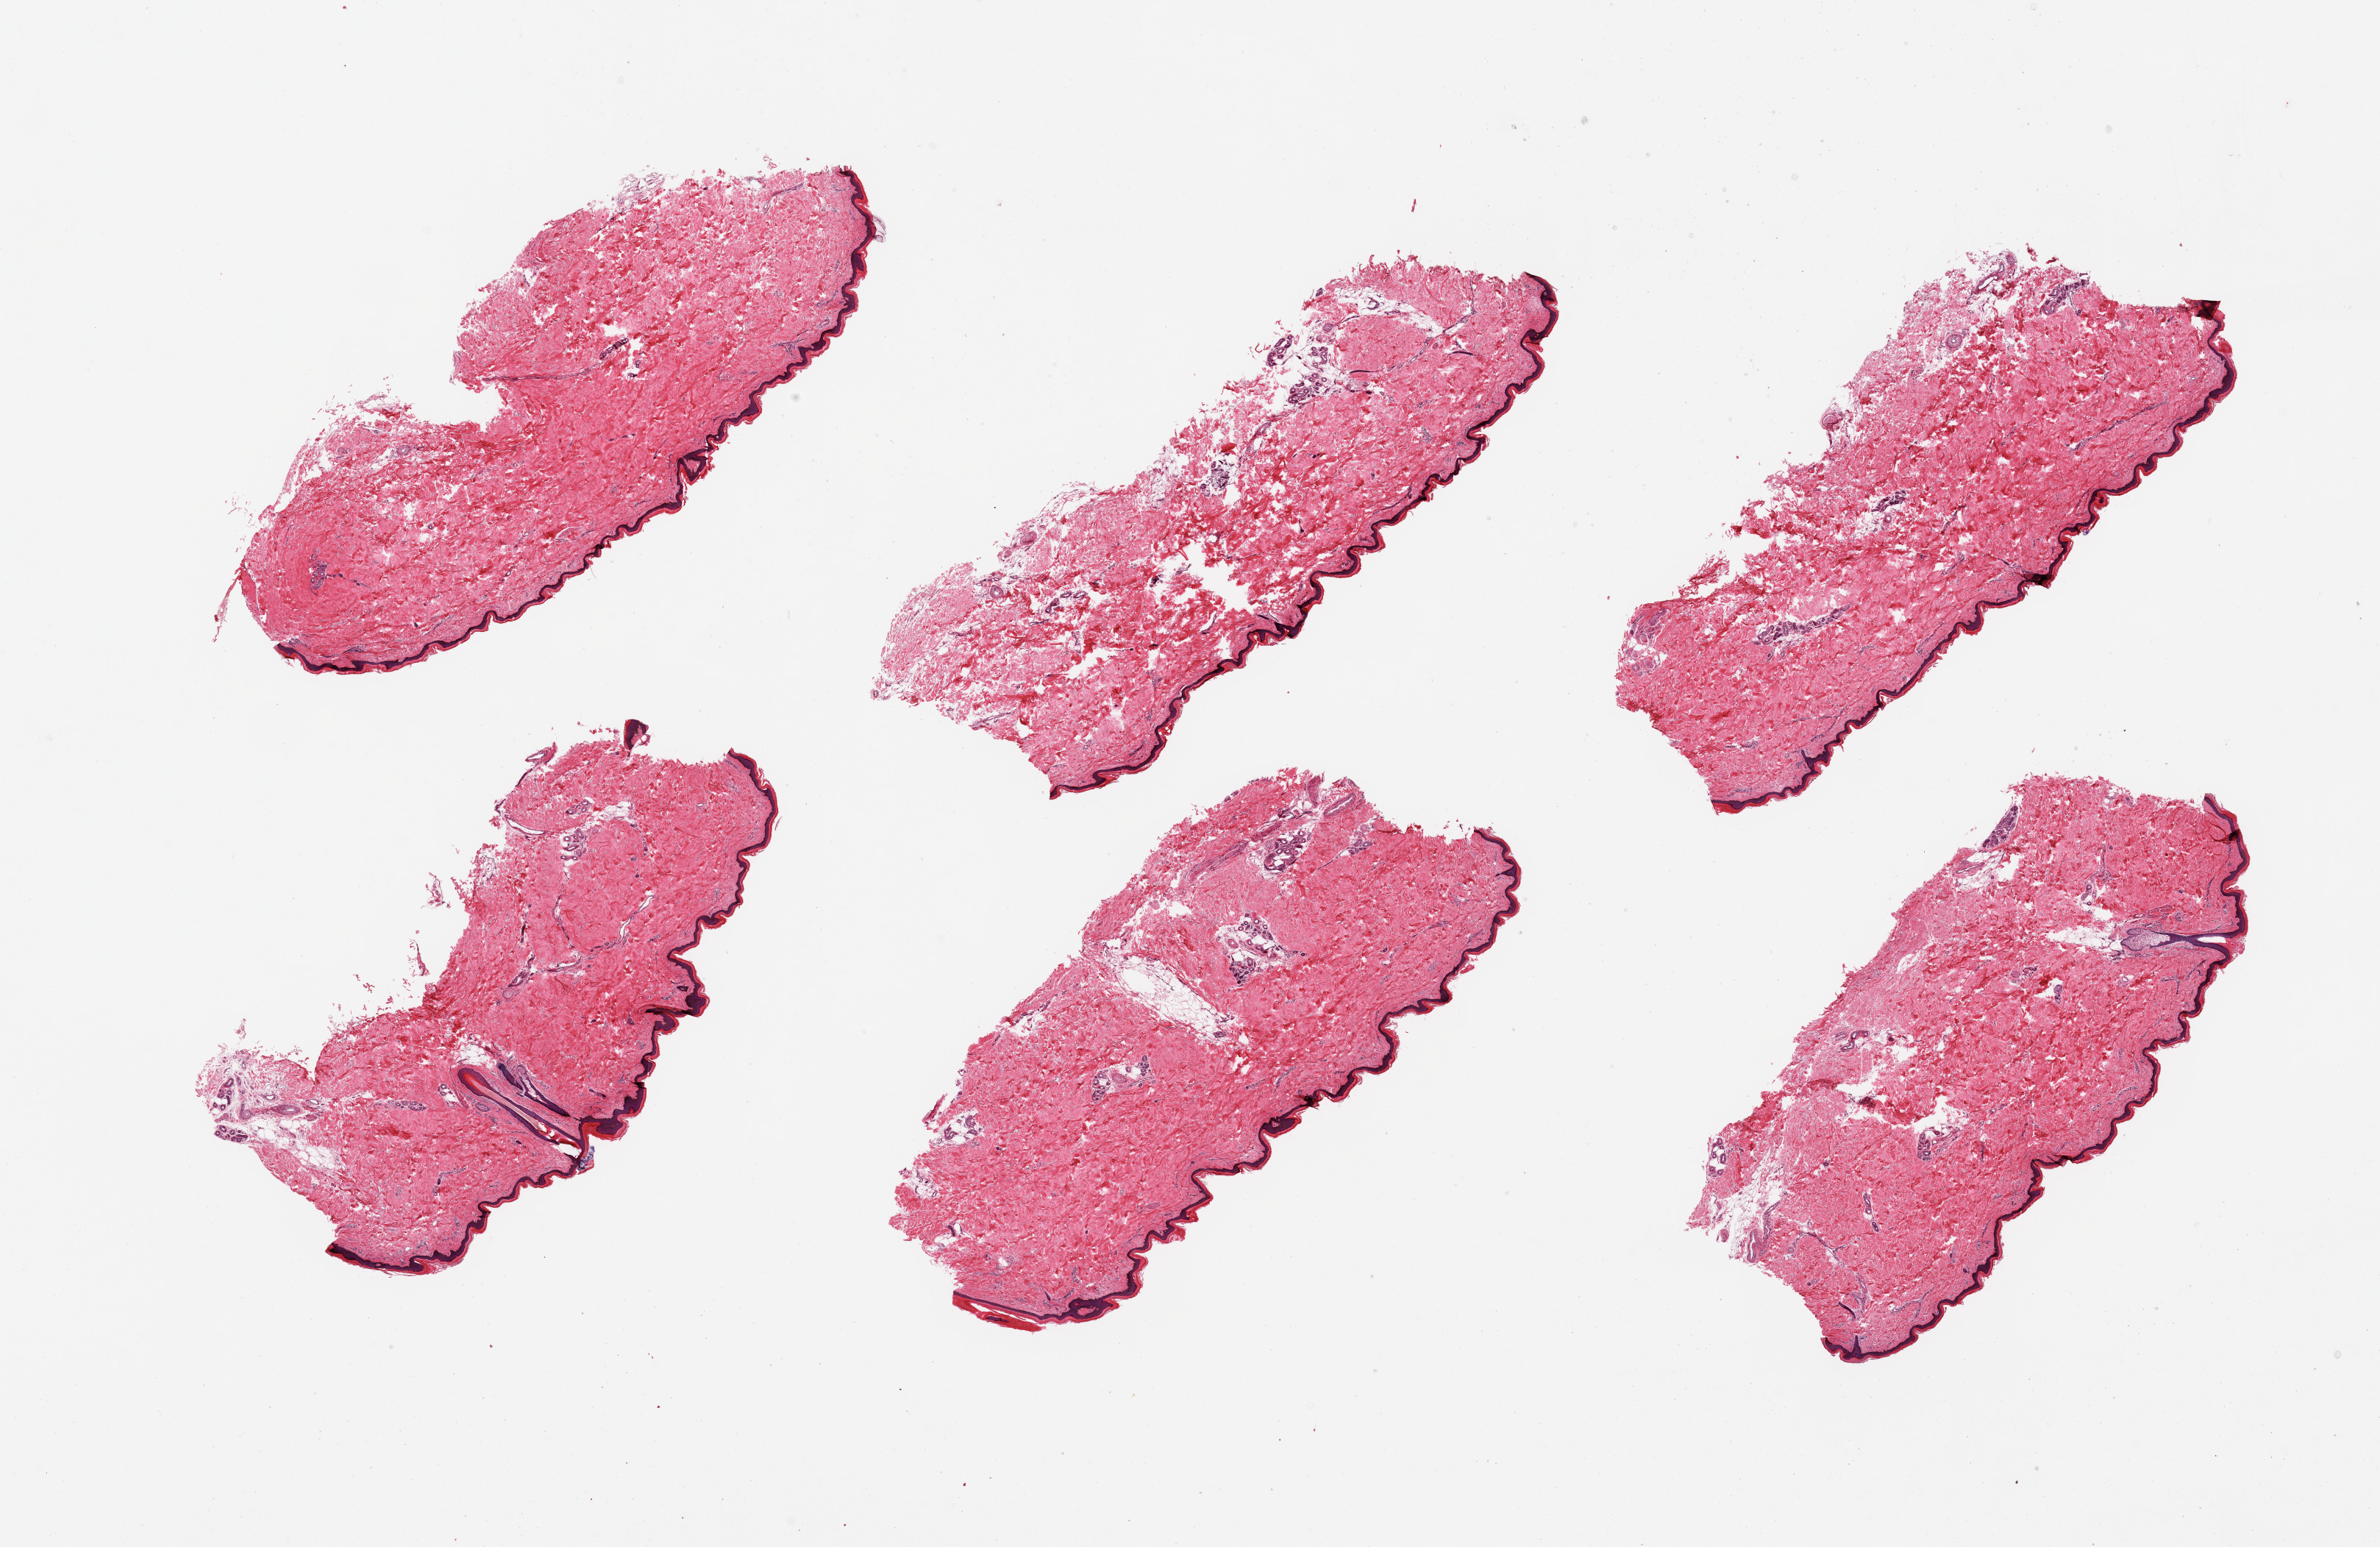
Whole-slide image, H&E stain — whole scanned area (about 25.6 x 16.6 mm, from a 20x scan) shown as a low-resolution overview. PAXgene-fixed paraffin-embedded (PFPE) section. Section of skin of lower leg (target tissue). Tissue donor sample. Donor: male.
- reviewer comment on this tissue sample: 6 pieces; ~10% internal fat (periadnexal), squamous epithelium ~ 32um